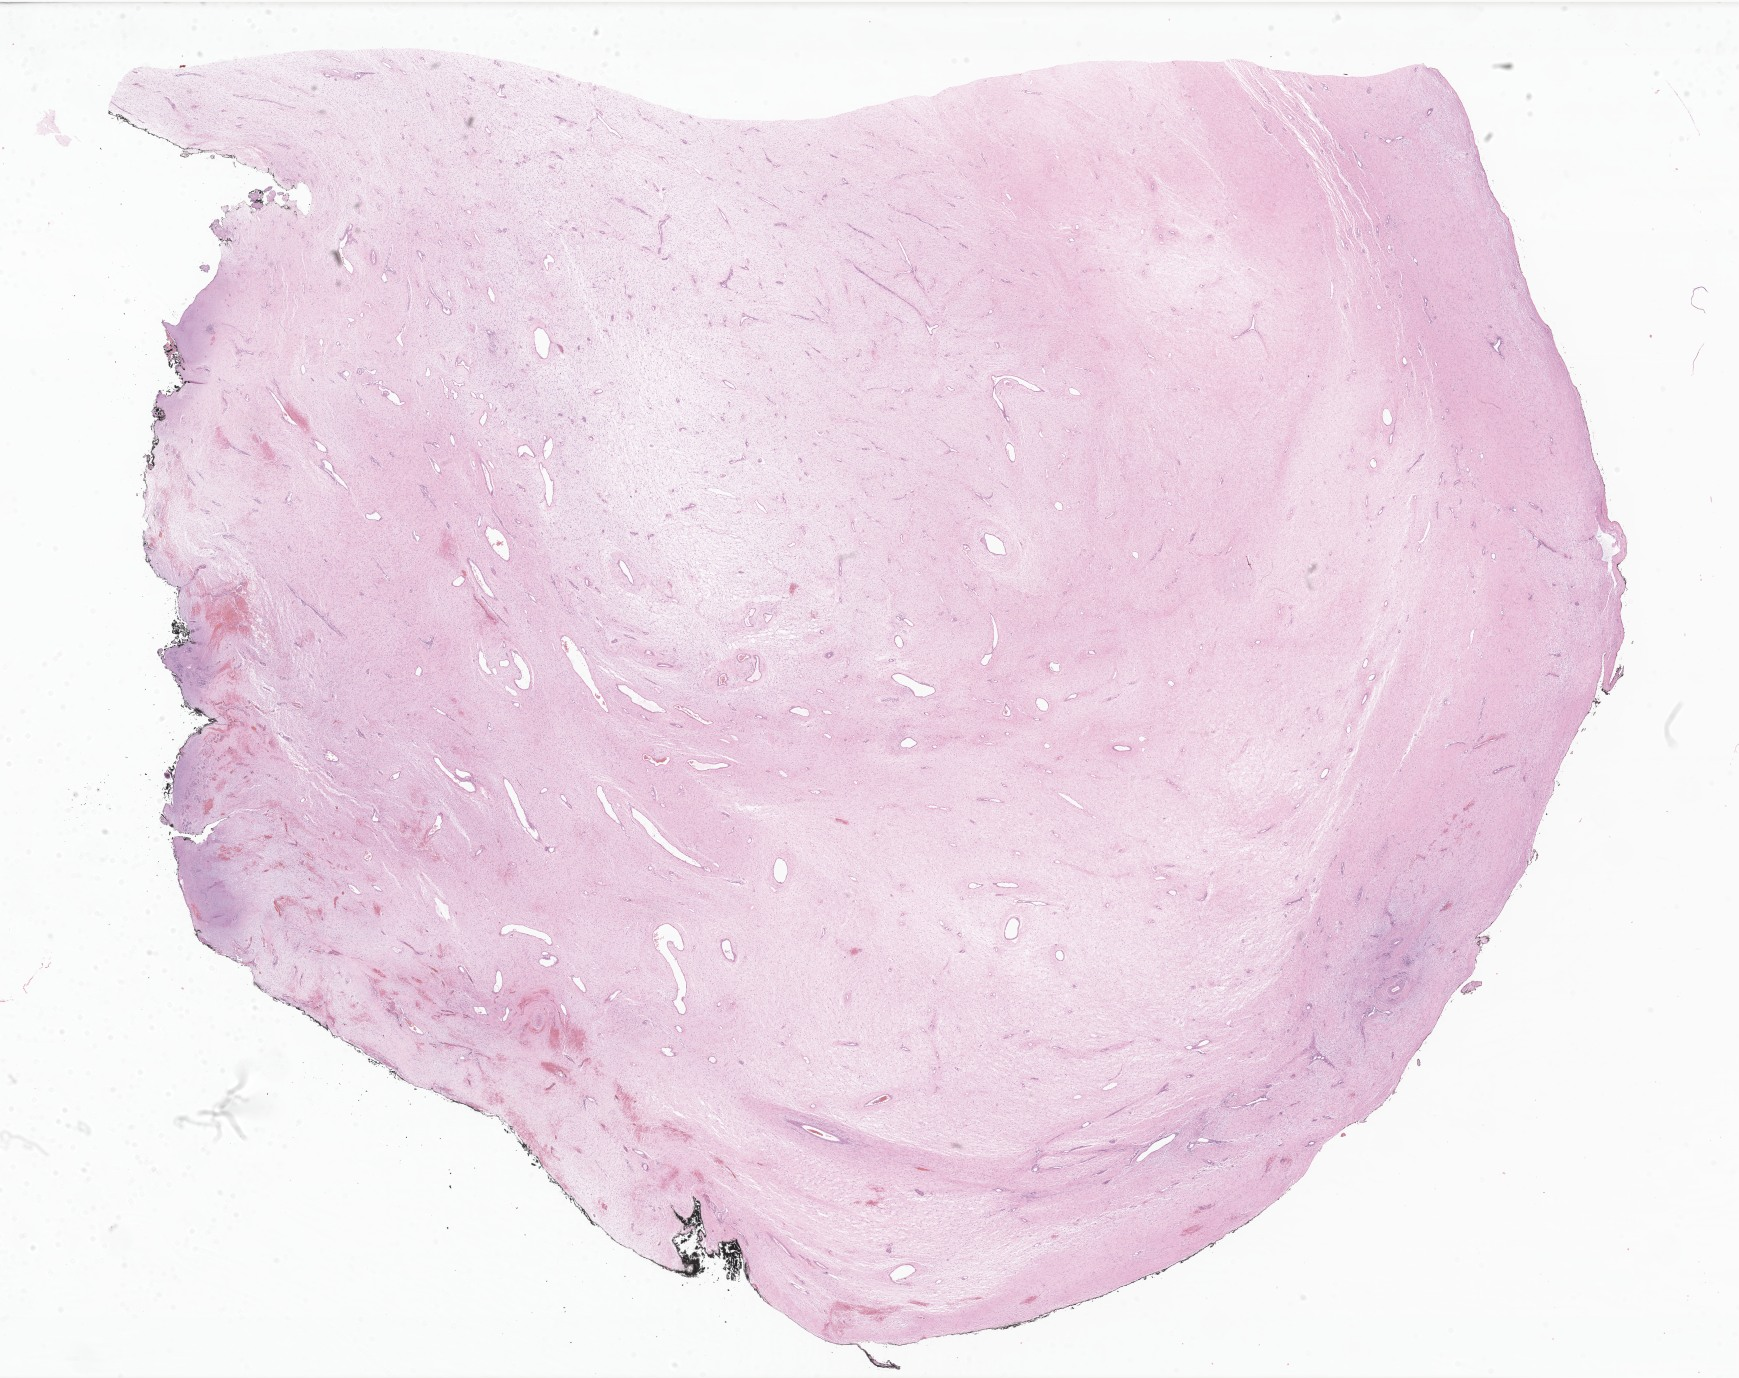
Digitized haematoxylin and eosin-stained section of tumor tissue from the pleura — whole scanned area (about 29.3 x 23.2 mm) shown as a low-resolution overview. Formalin-fixed, paraffin-embedded (FFPE) tissue. Patient: male, age 99 months (8 years 3 months).
* diagnosis: Sclerotic fibroma